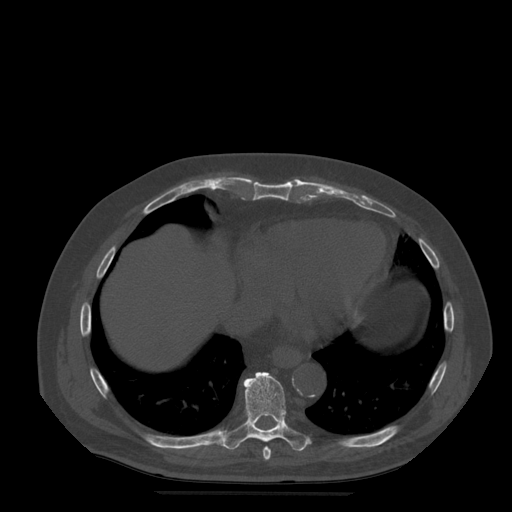
CT including the spine, one axial slice. Position 293 of 522 along the scan axis. Bone window (W 1800 / L 400 HU). 1.25 mm slice thickness. 512 × 512 image matrix, field of view 420 × 420 mm. Patient age 72 years. Case-level facts recorded for this patient, not image findings: primary cancer: prostate.
Structures marked on this image (semi-automatic segmentation, software-assisted and operator-edited):
- T8 vertebra: bounding box (x1, y1, x2, y2) in pixels: (263, 447, 272, 460)
- T9 vertebra: (222, 372, 310, 452)